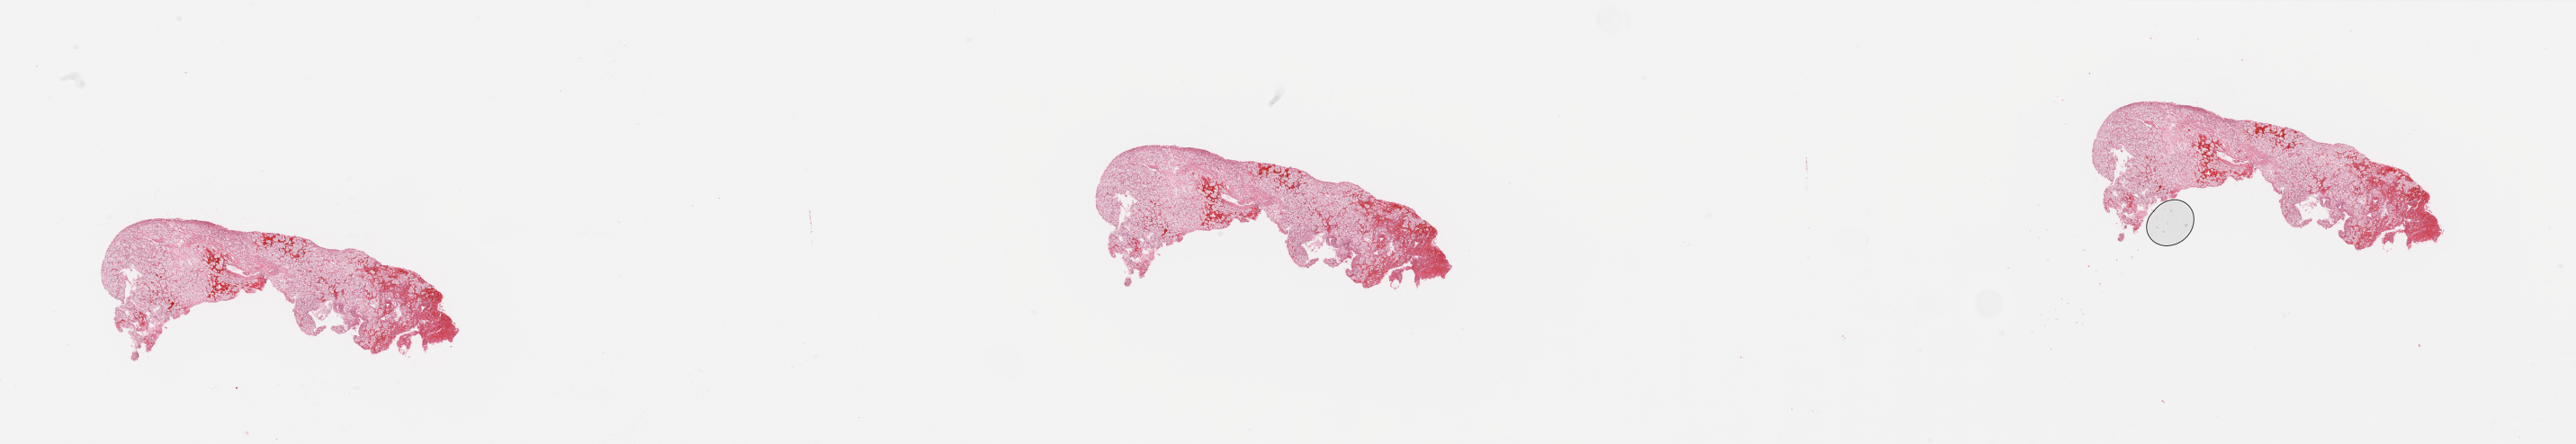
Digitized Hematoxylin and eosin (H&E) stained tissue section (whole slide) — shown as a low-resolution overview of the whole scanned area (about 45.3 x 7.8 mm), tumour tissue sample, sampled site: kidney. Male, 47 y/o. Histologic grade: G2 (moderately differentiated). Slide review estimates, as recorded: tumour nuclei 85%, necrosis 2%.
• diagnosis: Renal cell carcinoma, NOS
• primary tumour site (as recorded): upper pole
• AJCC pathologic stage: I